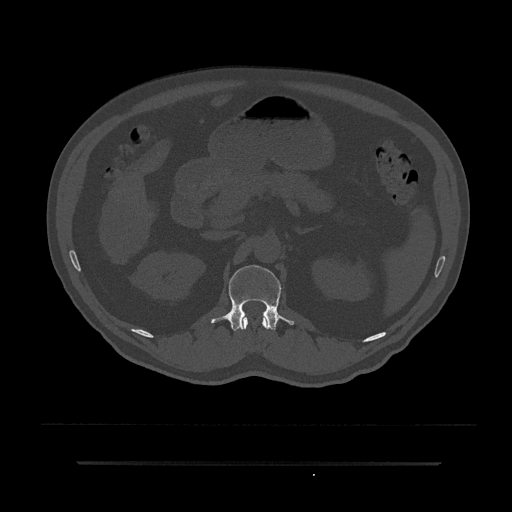
CT including the spine, one axial slice. Reconstruction kernel Br40s/3. Bone window (W 1800 / L 400 HU). 0.5 mm slice thickness. 512 × 512 image matrix, field of view 464 × 464 mm. Male patient, age 59 years. Case-level facts recorded for this patient, not image findings: primary cancer: bile ducts; vertebrae with lytic lesions (as recorded): T10.
Structures marked on this image (semi-automatically segmented with operator editing):
- L1 vertebra: box from (x=211, y=265) to (x=294, y=332) px
- T12 vertebra: (x=240, y=315)–(x=268, y=330)